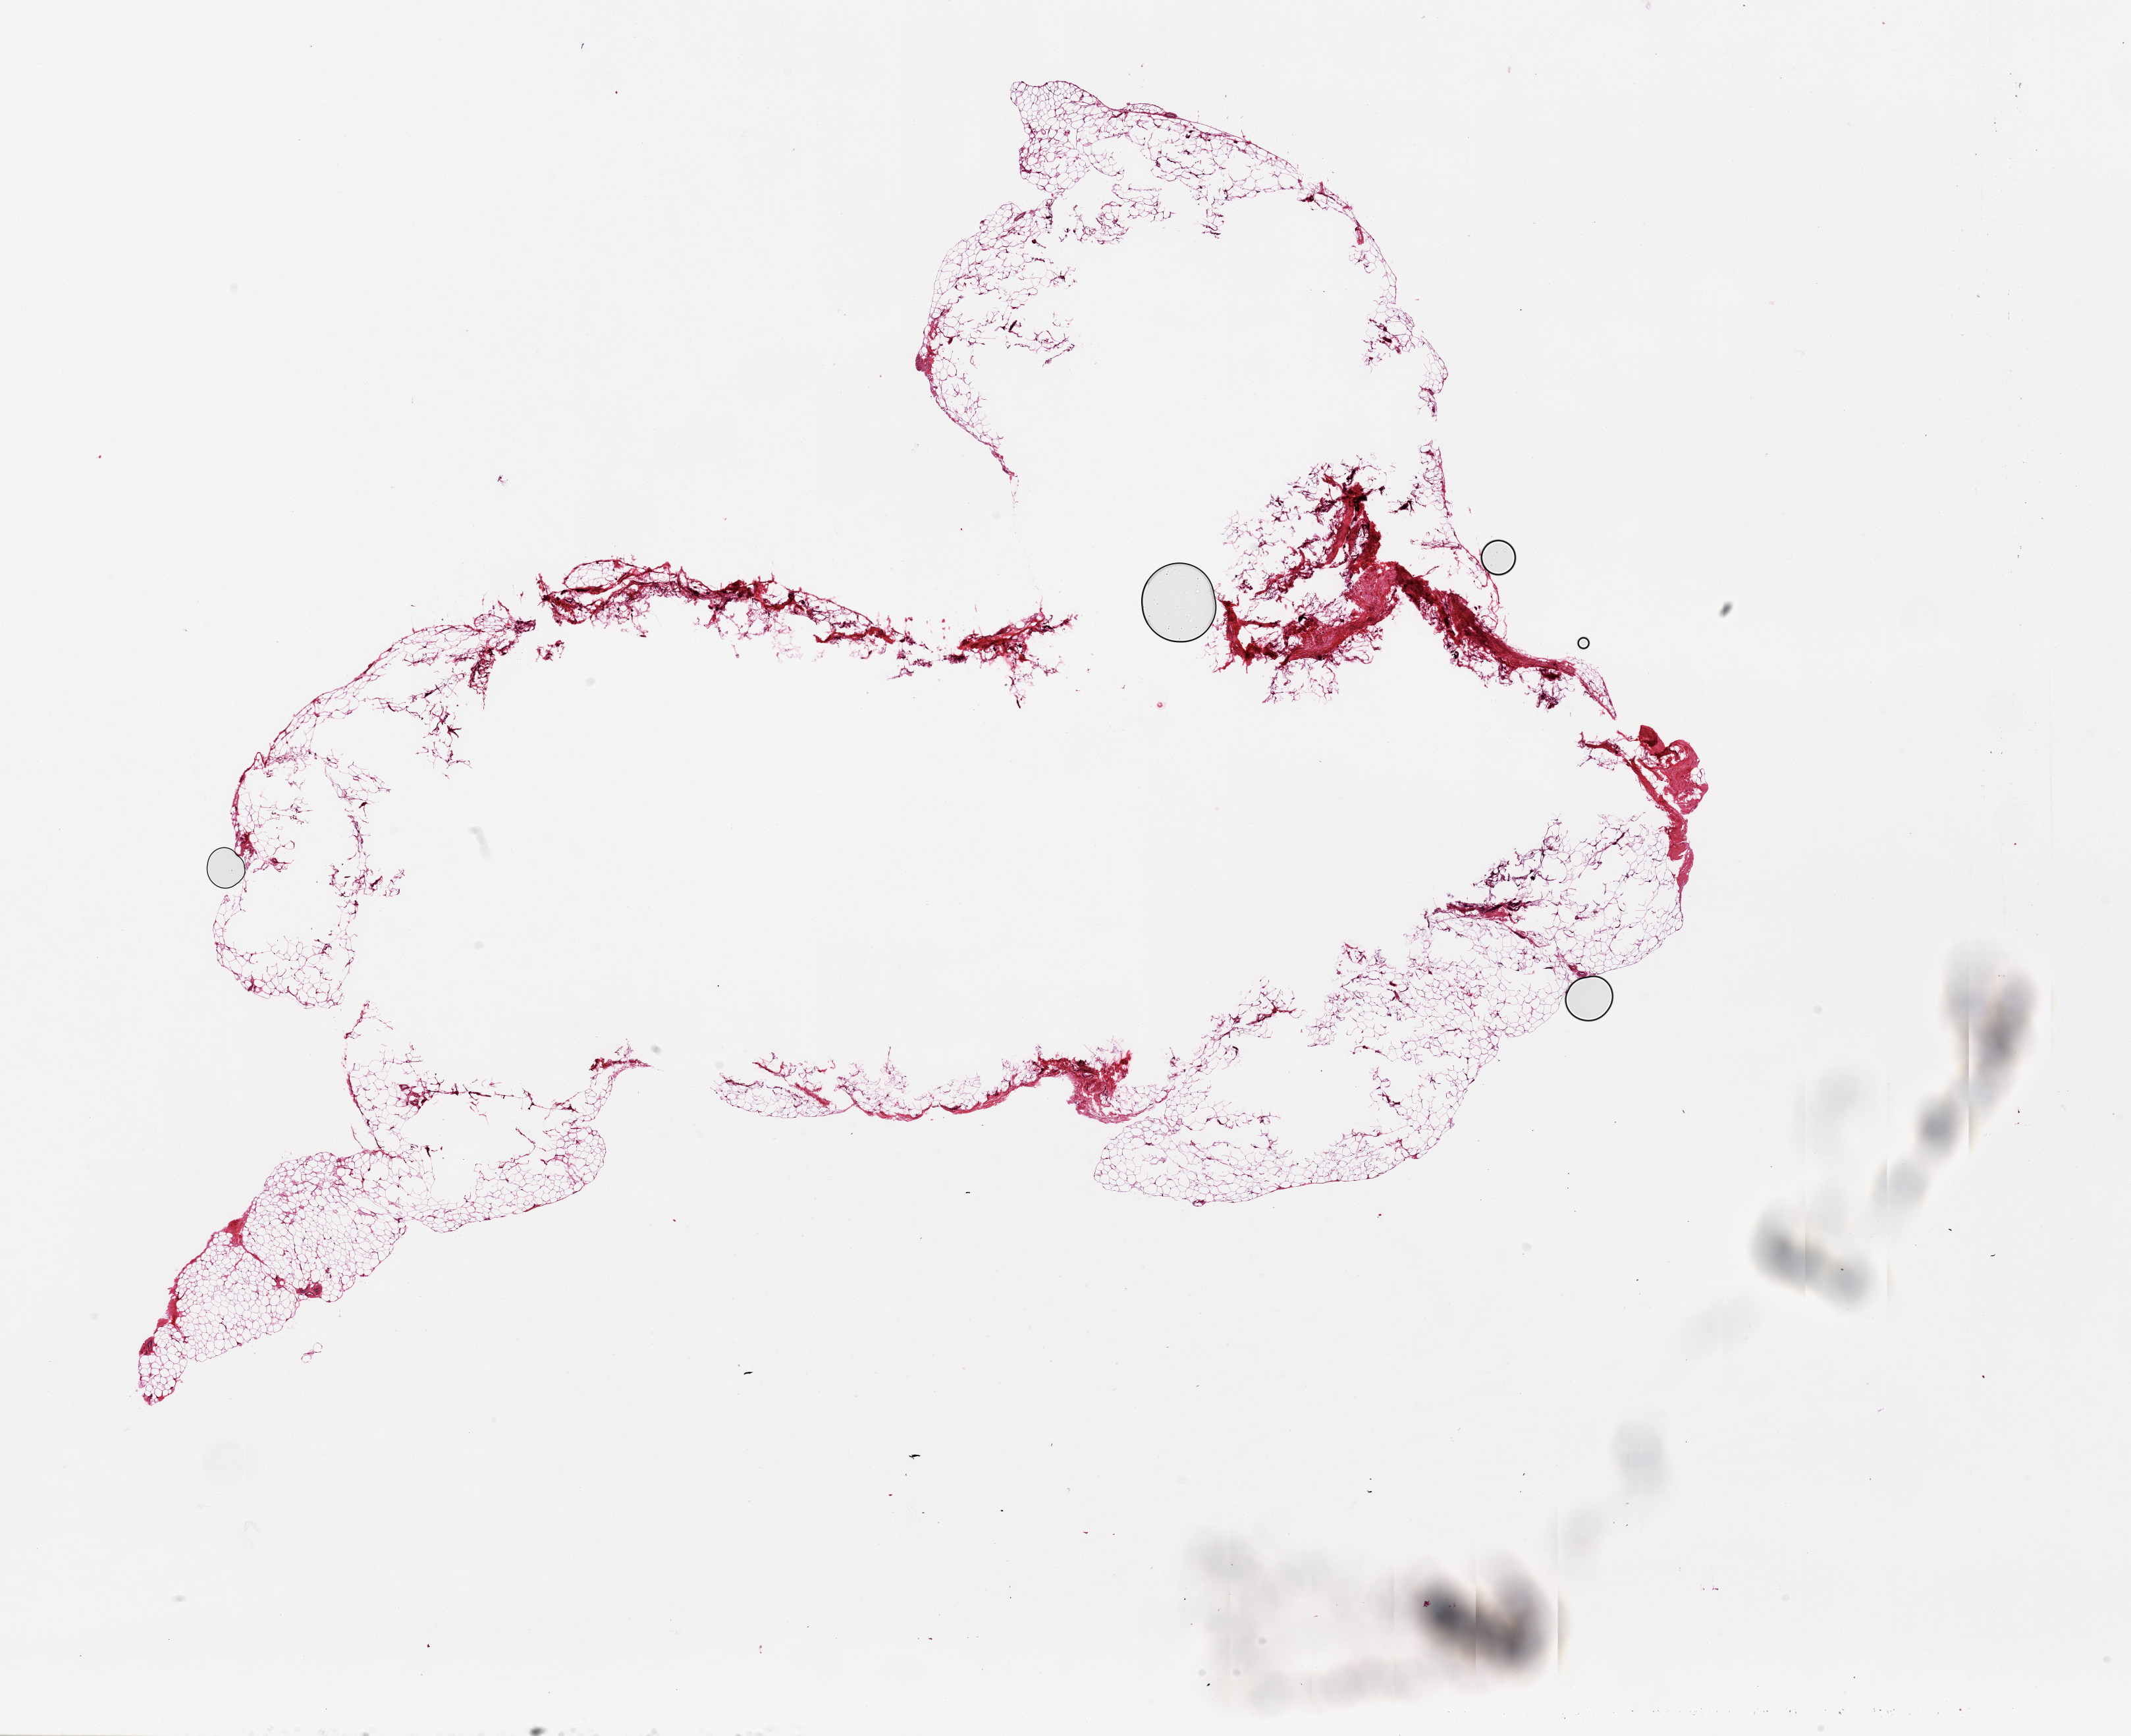
Whole-slide image, hematoxylin and eosin (H&E) stain, brightfield, shown as a low-resolution overview of the whole scanned area (about 25.6 x 20.8 mm, acquisition: 20x scan). PAXgene-fixed paraffin-embedded (PFPE) section. Target tissue: adipose tissue. Donor tissue sample. Male donor.
Pathologist's review note for this sample: Central 85% of specimen is unfixed and dropped out.